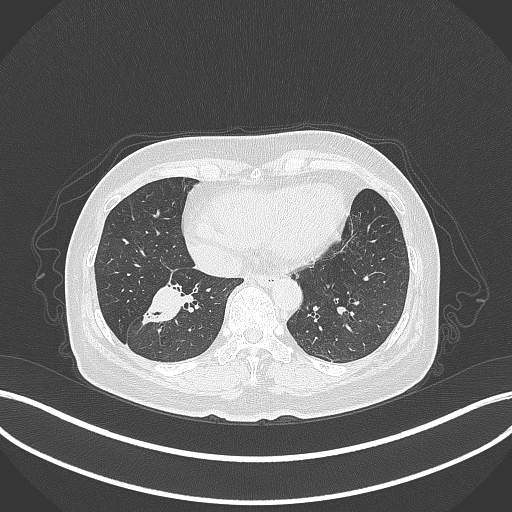
Chest CT, one axial slice. Slice 124 of 429 in the series (ordered by position). Reconstruction kernel B70f. 120 kVp. Lung window (W 1500 / L -600 HU). 1 mm slice thickness. 512 × 512 image matrix, field of view 400 × 400 mm. Patient: female, 67 years. From the clinical record (not read from this slice): clinical TNM (as recorded): T1c N1 M0.
Outlined on this slice (rectangle marked by the reading radiologist):
- lung tumour (recorded histology: adenocarcinoma): bounding box (x1, y1, x2, y2) in pixels: (135, 278, 190, 331)